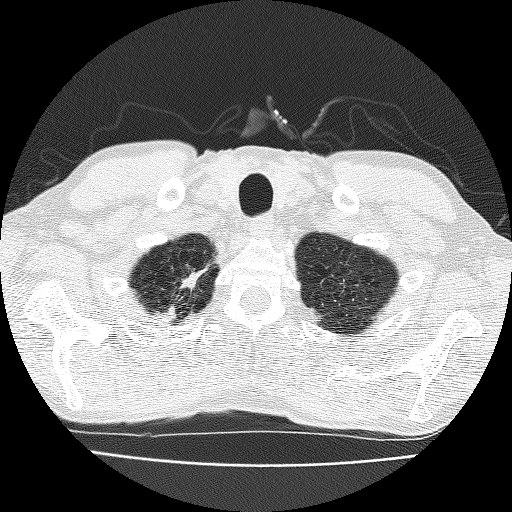
Low-dose screening chest CT, one axial slice; slice 162 of 185 in the series (ordered by position); reconstruction kernel FC51; 120 kVp; lung window (W 1500 / L -600 HU); 2 mm slice thickness; 512 × 512 image matrix.
Structures marked on this image (manually delineated by an expert):
- lesion 1 (nodule, upper lobe of right lung): bounding box (x1, y1, x2, y2) in pixels: (182, 269, 206, 289)